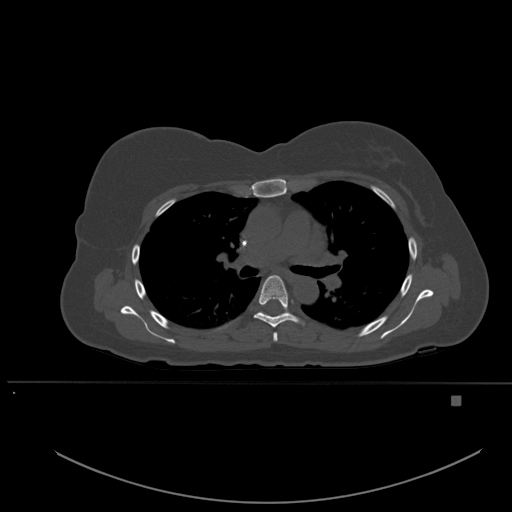
CT including the spine, one axial slice; slice 365 of 651 in the series (ordered by position); bone window (W 1800 / L 400 HU); 1.5 mm slice thickness; 512 × 512 image matrix, field of view 443 × 443 mm. Patient: female, 49 years. From the clinical record (not read from this slice): primary cancer: breast.
Structures marked on this image (semi-automatically segmented with operator editing):
- T4 vertebra: box from (x=273, y=332) to (x=278, y=342) px
- T5 vertebra: (x=254, y=275)–(x=304, y=328)